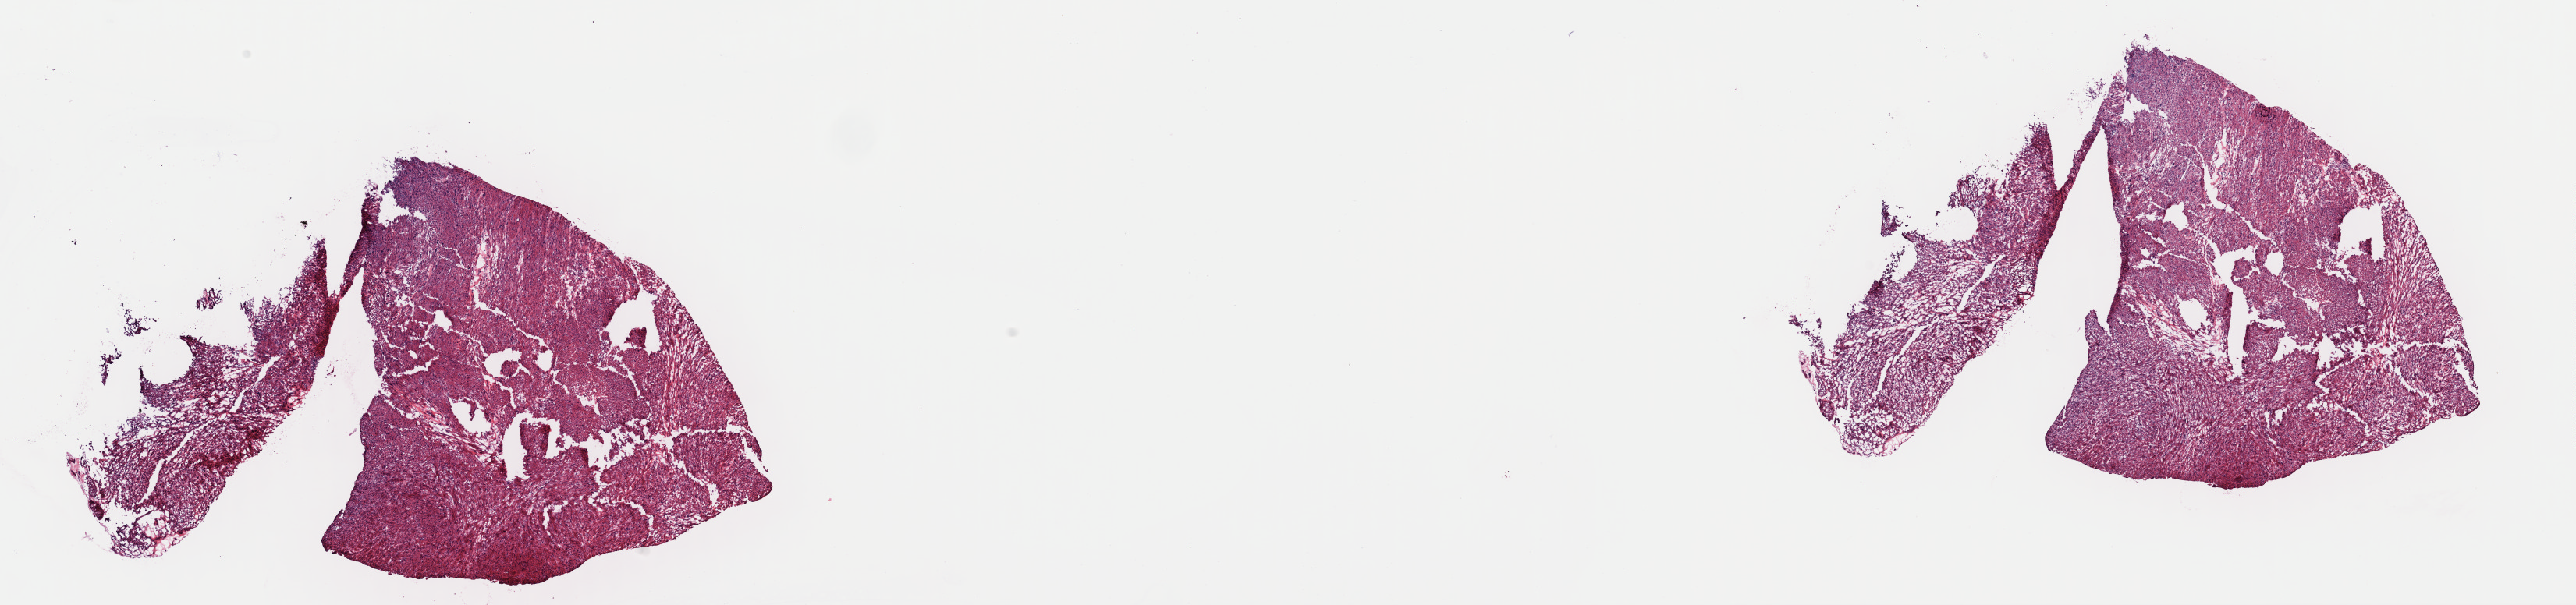
H&E whole-slide image, whole scanned area (about 26.1 x 6.1 mm, from a 40x scan) shown as a low-resolution overview, frozen section from the top of the tissue portion, sample: primary tumour, uterus. Patient: female, age at initial diagnosis 49 years. Pathologist review of this section (percent, as recorded): tumour cells 100%, tumour nuclei 95%, normal cells 0%, stromal cells 0%, necrosis 0%. Infiltration values recorded for this section: lymphocyte infiltration 0%, monocyte infiltration 0%, neutrophil infiltration 0%.
Diagnosis: Leiomyosarcoma, NOS.